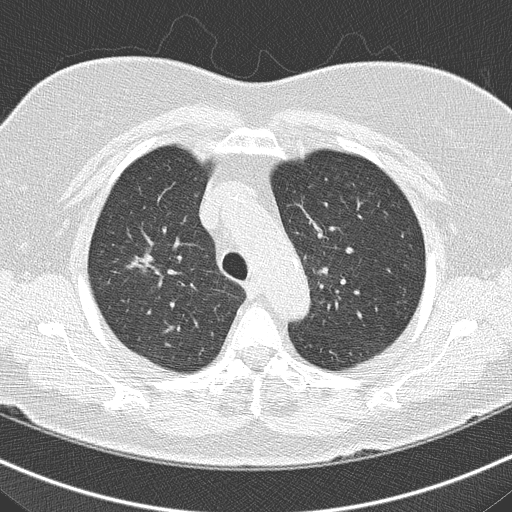
Axial slice from a low-dose chest CT screening exam. Third screening round (two years after baseline). Lung window (W 1500 / L -600 HU). 2 mm slice thickness. Lung (sharp) reconstruction kernel (B50f). Slice 134 of 161 in the series. 512 × 512 image matrix, field of view 316 × 316 mm. Female, age 74 years at enrolment. Former smoker at enrolment.
Expert reader's lesion annotation, bounding box (x1, y1, x2, y2) in pixels: (111, 235, 179, 297). The screening reader recorded 5 non-calcified nodules or masses ≥4 mm on this exam; which of them this box marks is not recorded. Official screen result: positive, other. Lung cancer was diagnosed 117 days after this screen: bronchiolo-alveolar carcinoma, non-mucinous, right upper lobe, well differentiated (G1), stage IA (AJCC 6th edition), 14 mm at pathology.